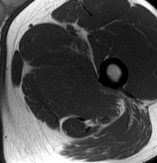
MRI of an extremity soft-tissue mass, one axial slice; slice 62 of 70 in the series (ordered by position); MR volume resampled by the dataset authors to the PET/CT grid (not the native acquisition matrix); 3.27 mm slice thickness; 157 × 163 image matrix, field of view 153 × 159 mm. Male patient. Case-level facts recorded for this patient, not image findings: histological type: extraskeletal osteosarcoma; grade: high; site of the primary tumour: left adductur.
Annotated regions visible in this slice (expert contour drawn on MRI and transferred to this co-registered scan by the dataset authors):
- gross tumour volume (mass): bounding box <31,35,123,125> (left, top, right, bottom; pixels)